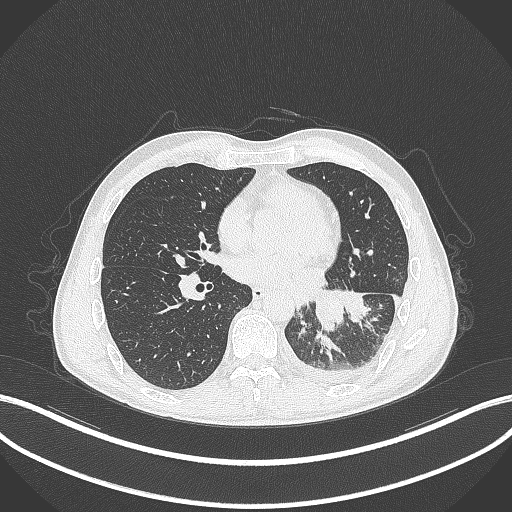
Chest CT, one axial slice; slice 135 of 295 in the series (ordered by position); reconstruction kernel B70f; lung window (W 1500 / L -600 HU); 1 mm slice thickness; 512 × 512 image matrix, field of view 400 × 400 mm. Patient: male, 47 years. Case-level facts recorded for this patient, not image findings: clinical TNM (as recorded): T3 N1 M1c; histopathological grade: G3.
Outlined on this slice (rectangle marked by the reading radiologist):
- lung tumour (recorded histology: small cell carcinoma): bounding box (x1, y1, x2, y2) in pixels: (309, 287, 344, 333)